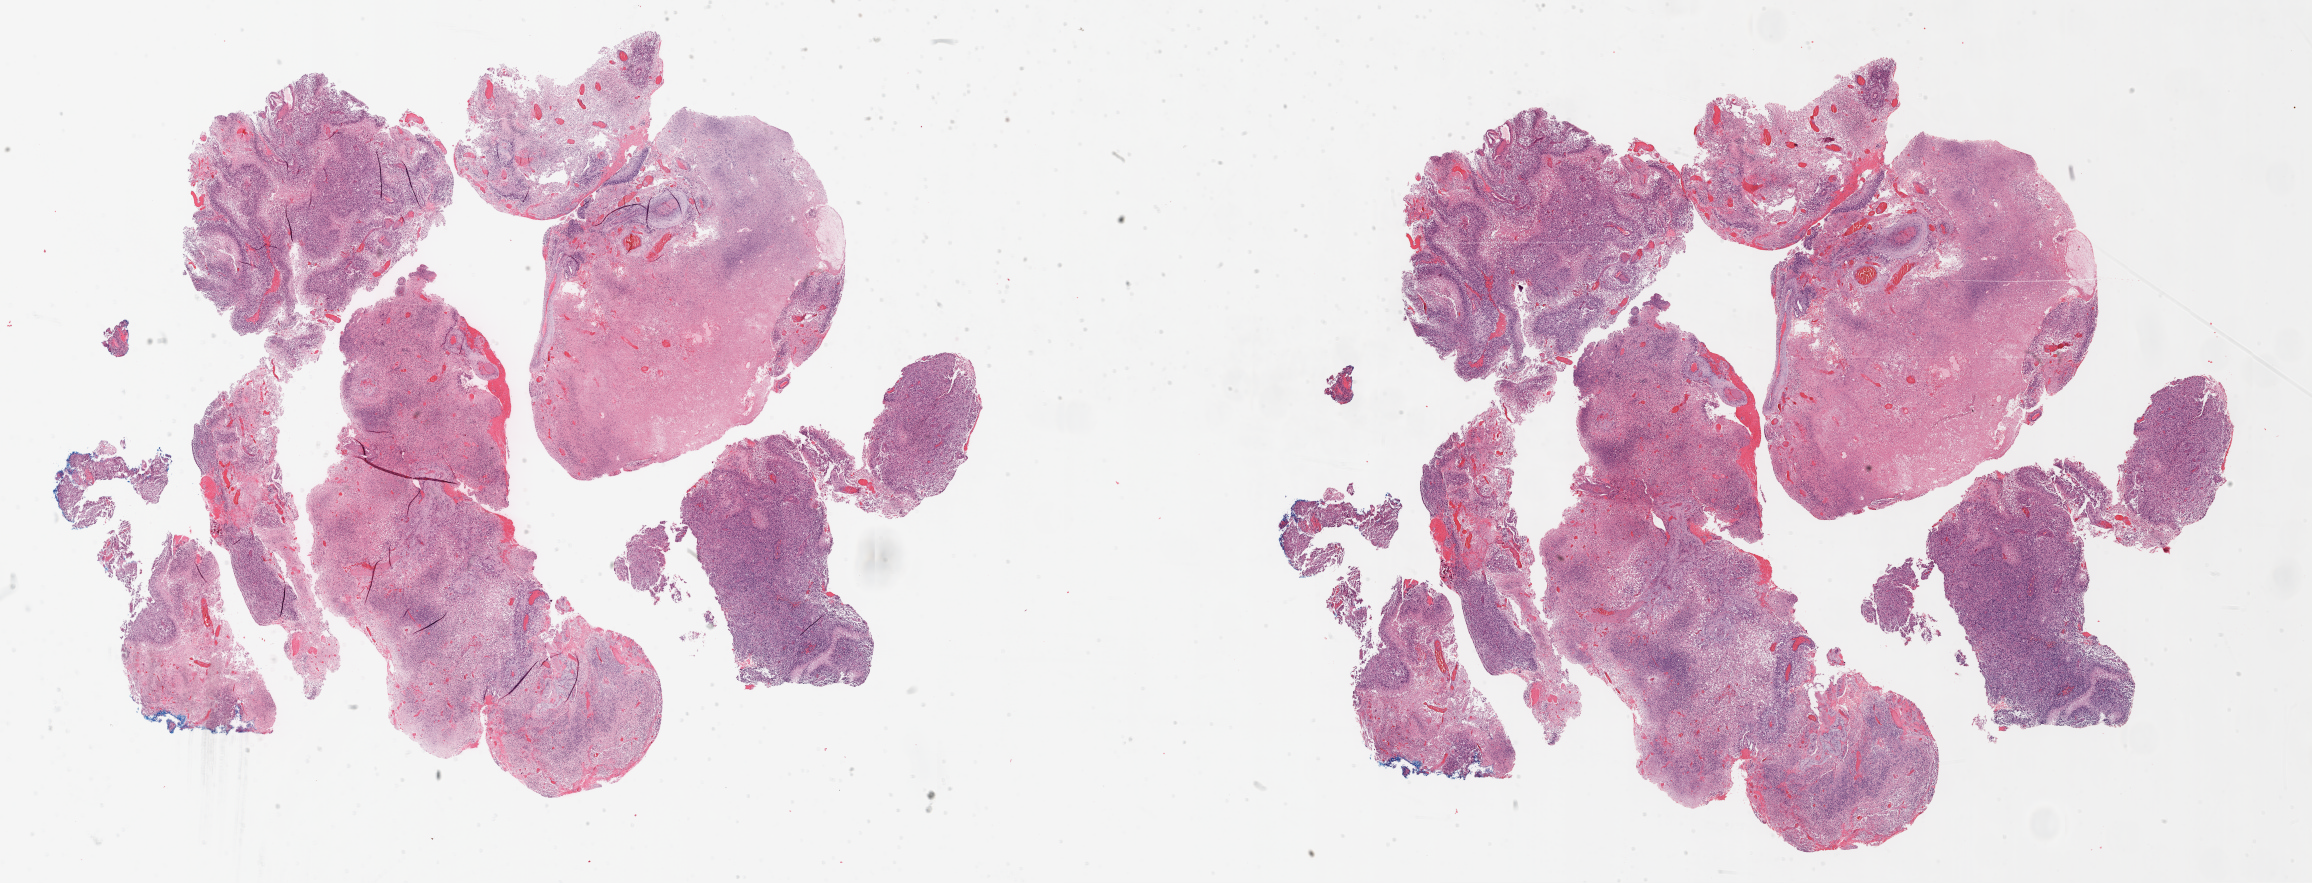
H&E whole-slide image — shown as a low-resolution overview of the whole scanned area (about 37.1 x 14.2 mm, from a 20x scan); formalin-fixed paraffin-embedded (FFPE) diagnostic section; sample: primary tumour, brain. Patient: male, age at initial diagnosis 66 years.
Pathologic diagnosis: Glioblastoma.